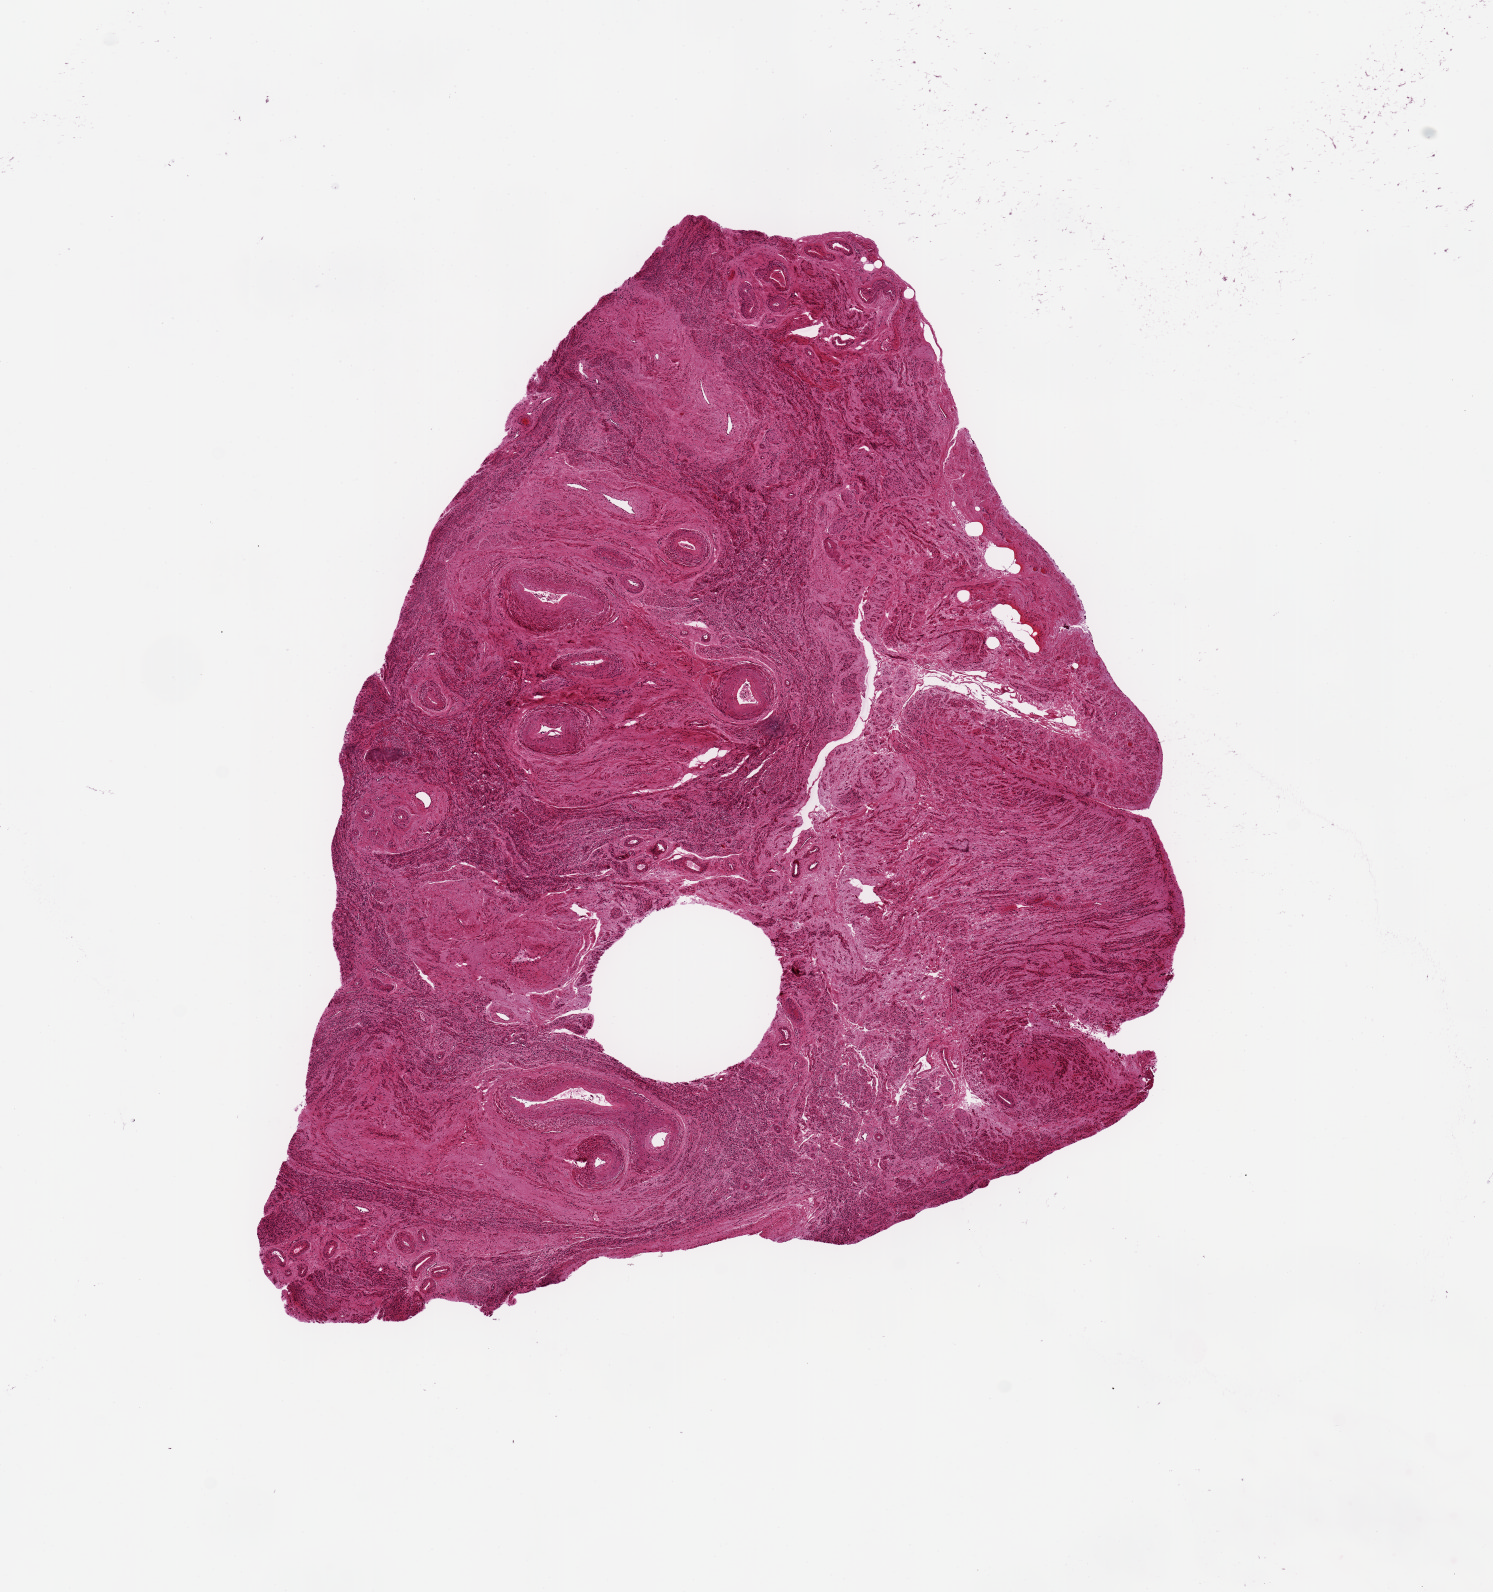
Whole-slide image, hematoxylin and eosin (H&E) stain, brightfield, whole scanned area (about 11.8 x 12.6 mm) shown as a low-resolution overview.
• specimen: PAXgene-fixed, paraffin-embedded tissue; target tissue: endocervix; donor tissue sample